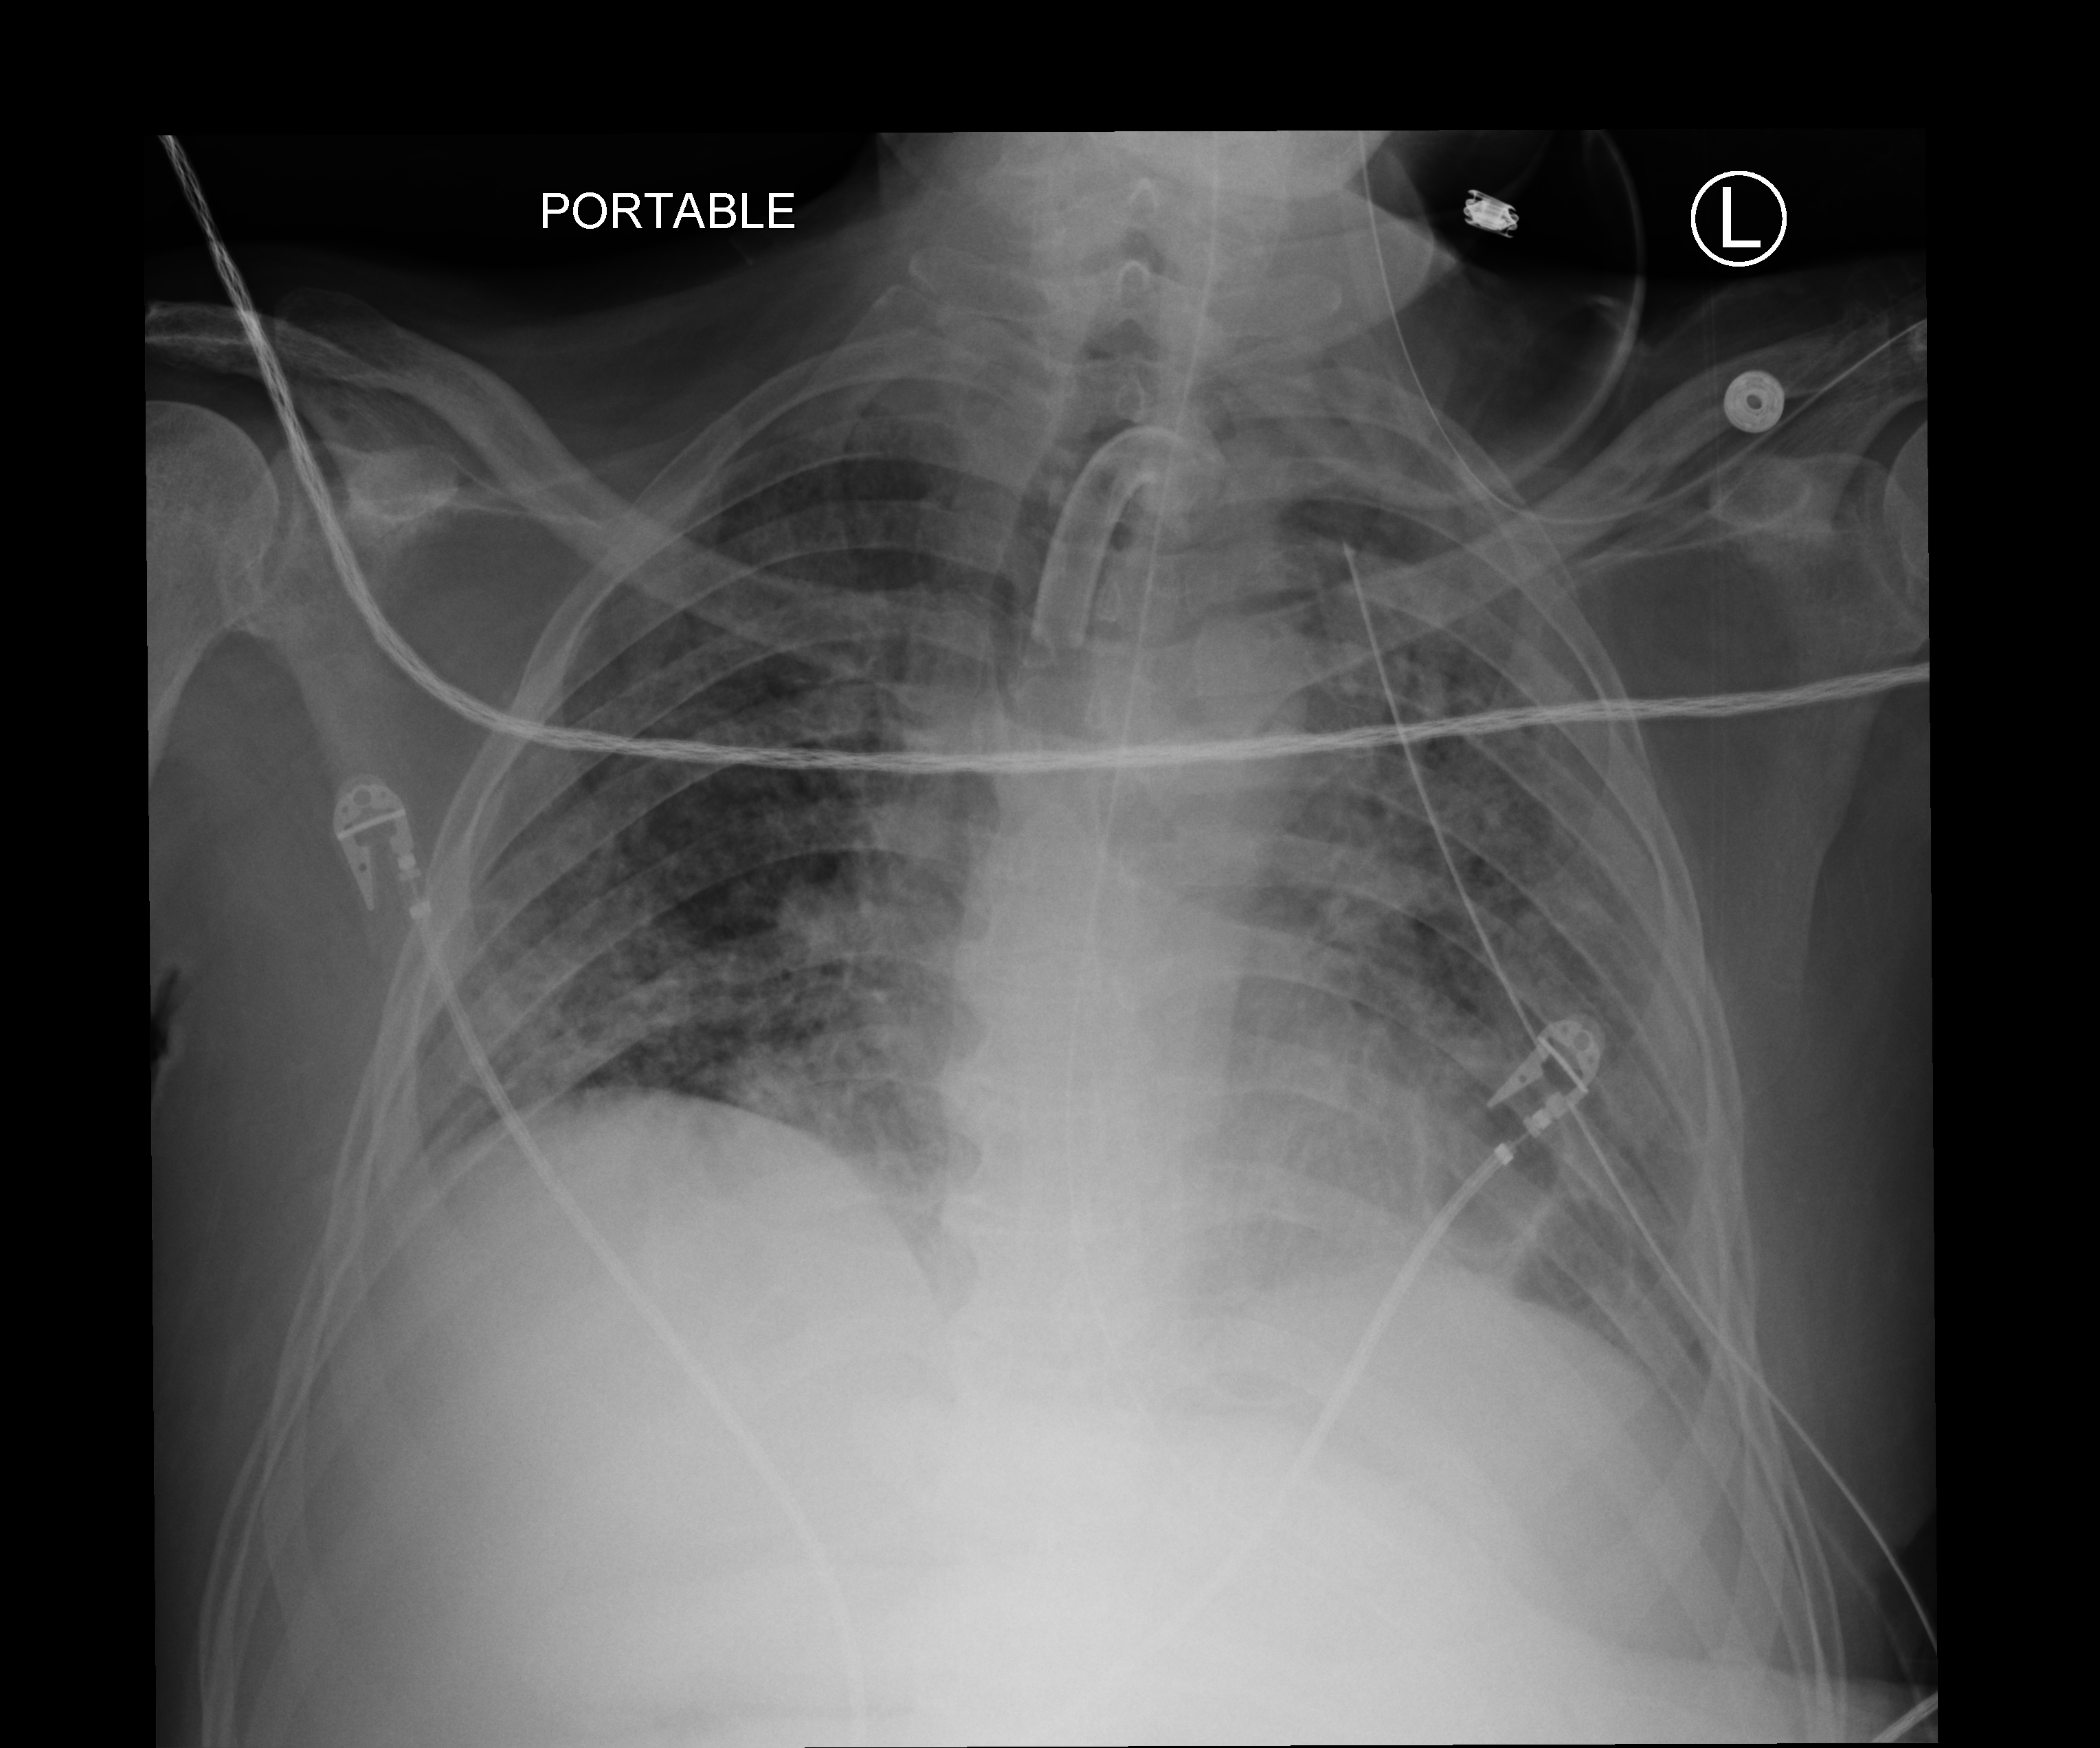
Bedside chest radiograph (computed radiography); anteroposterior (AP) projection. Male patient hospitalised with COVID-19, age 18–59 years.
Hospital-stay facts (about this admission, not read from this image; timing relative to this image not recorded): mechanically ventilated during this hospital stay: yes; admitted to intensive care during this hospital stay: yes.